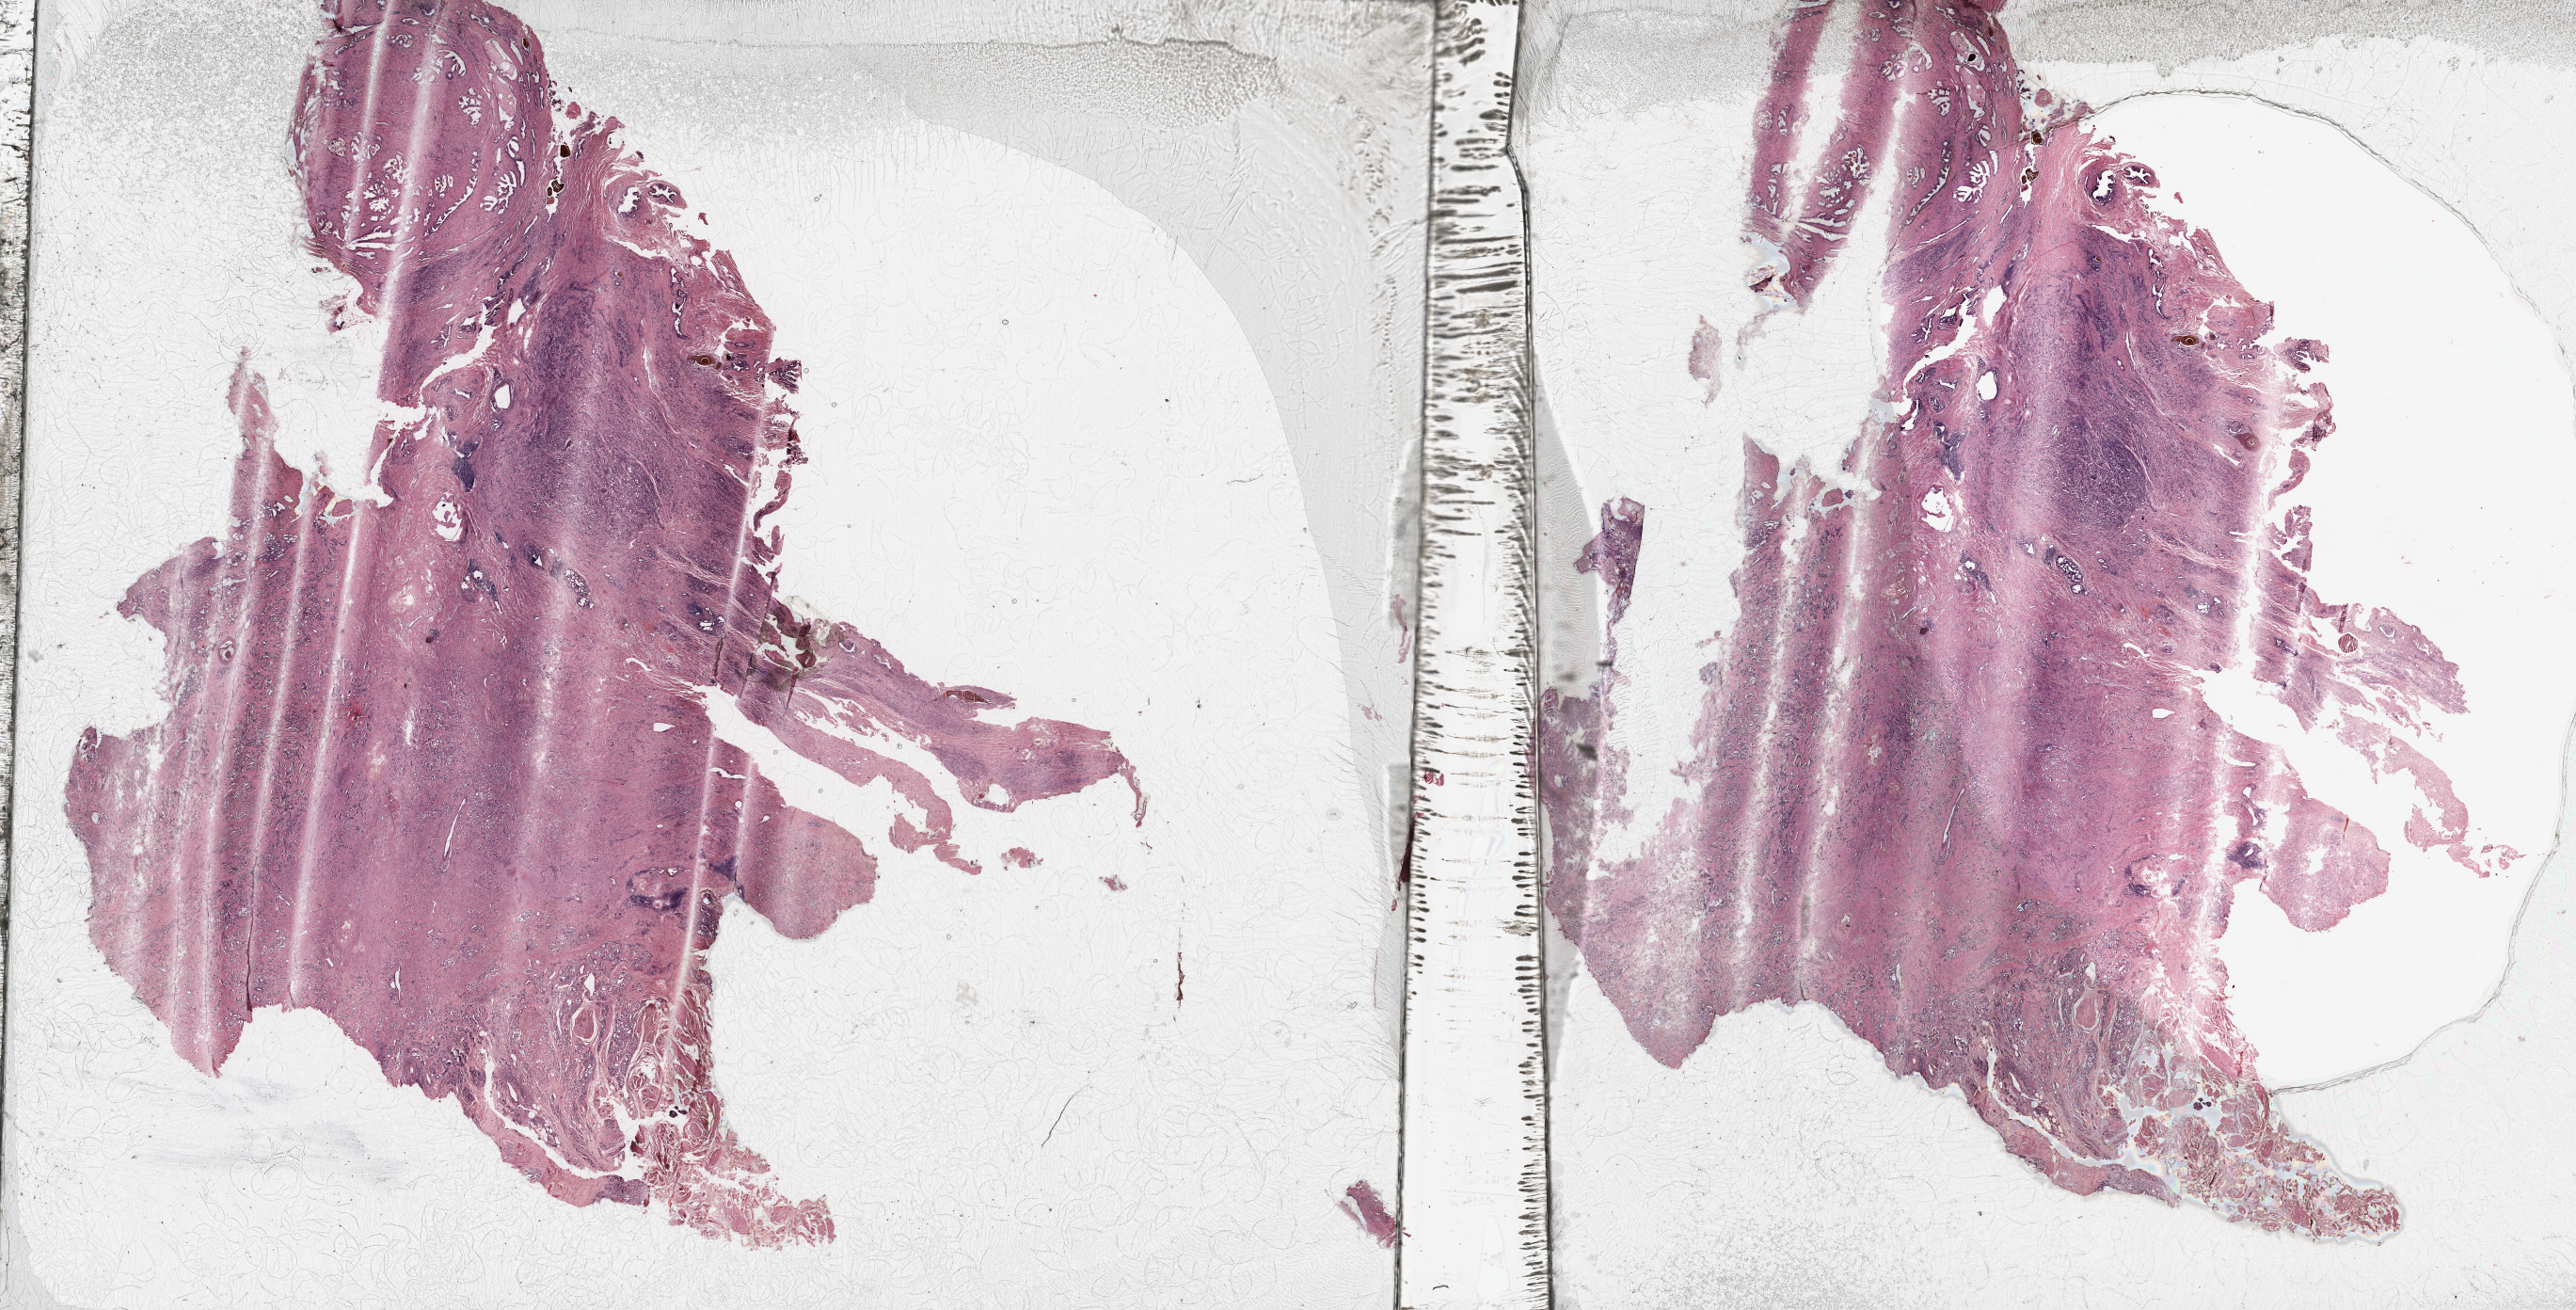
H&E whole-slide image, a low-resolution overview of the entire scanned area, about 44.3 x 22.5 mm; FFPE section; primary tumour sample from the prostate. Patient: male, age at initial diagnosis 73 years. Gleason score: 7 (3+4).
Laterality: right. Histologic diagnosis: Adenocarcinoma, NOS.